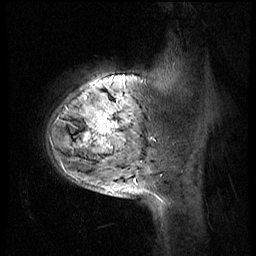
Breast MRI (dynamic contrast-enhanced), one sagittal slice; slice 10 of 56 in the series (ordered by position); 4 images stored at this slice position (order not interpretable as contrast timing); 1.5 T; TE 4.2 ms, TR 8.9 ms; 256 × 256 image matrix, field of view 220 × 220 mm. Female patient, age 51 years. From the clinical record (not read from this slice): setting: breast cancer imaged before/during neoadjuvant chemotherapy; receptor status: triple-negative.
Outlined on this slice (semi-automatic segmentation, software-assisted and operator-edited):
- analysis volume of interest (the breast-tissue region the enhancement analysis was run in; not a lesion): bounding box [x1, y1, x2, y2] px = [43, 70, 150, 173]
- tumour enhancement mask (voxels above the 140 % enhancement threshold inside the analysis volume of interest): [87, 112, 114, 147]